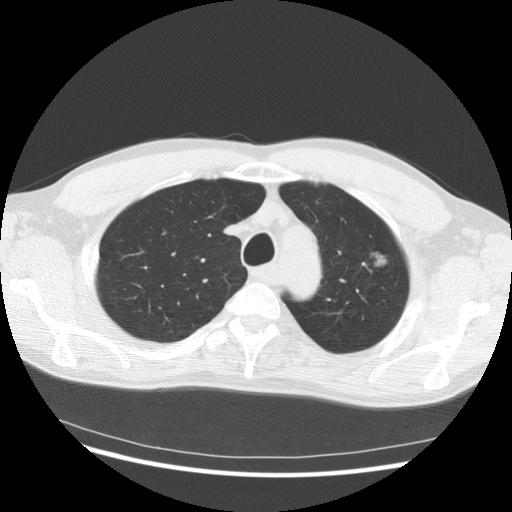
Chest CT (low-dose screening protocol), one axial image. Third screening round (two years after baseline). Lung window (W 1500 / L -600 HU). 140 kVp. Slice 113 of 145 in the series. Male, age 61 years at enrolment. Former smoker at enrolment.
• Expert reader's lesion annotation, bounding box [x1, y1, x2, y2] px = [330, 240, 404, 321].
• Screening reader's record for this exam (one nodule recorded; not confirmed to be the boxed lesion): non-calcified nodule or mass ≥4 mm, left upper lobe, 37 × 33 mm, poorly defined margins, mixed attenuation, pre-existing on the prior screen: yes; interval growth: yes.